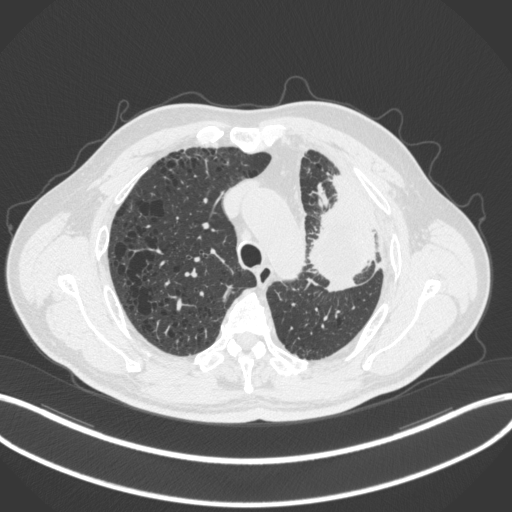
Chest CT, one axial slice. Slice 224 of 286 in the series (ordered by position). Reconstruction kernel B31f. Lung window (W 1500 / L -600 HU). 1 mm slice thickness. 512 × 512 image matrix, field of view 400 × 400 mm. Male patient, age 68 years. Case-level facts recorded for this patient, not image findings: clinical TNM (as recorded): T3 N3 M1.
Outlined on this slice (rectangle marked by the reading radiologist):
- lung tumour (recorded histology: adenocarcinoma): bounding box [x1, y1, x2, y2] px = [305, 169, 380, 289]